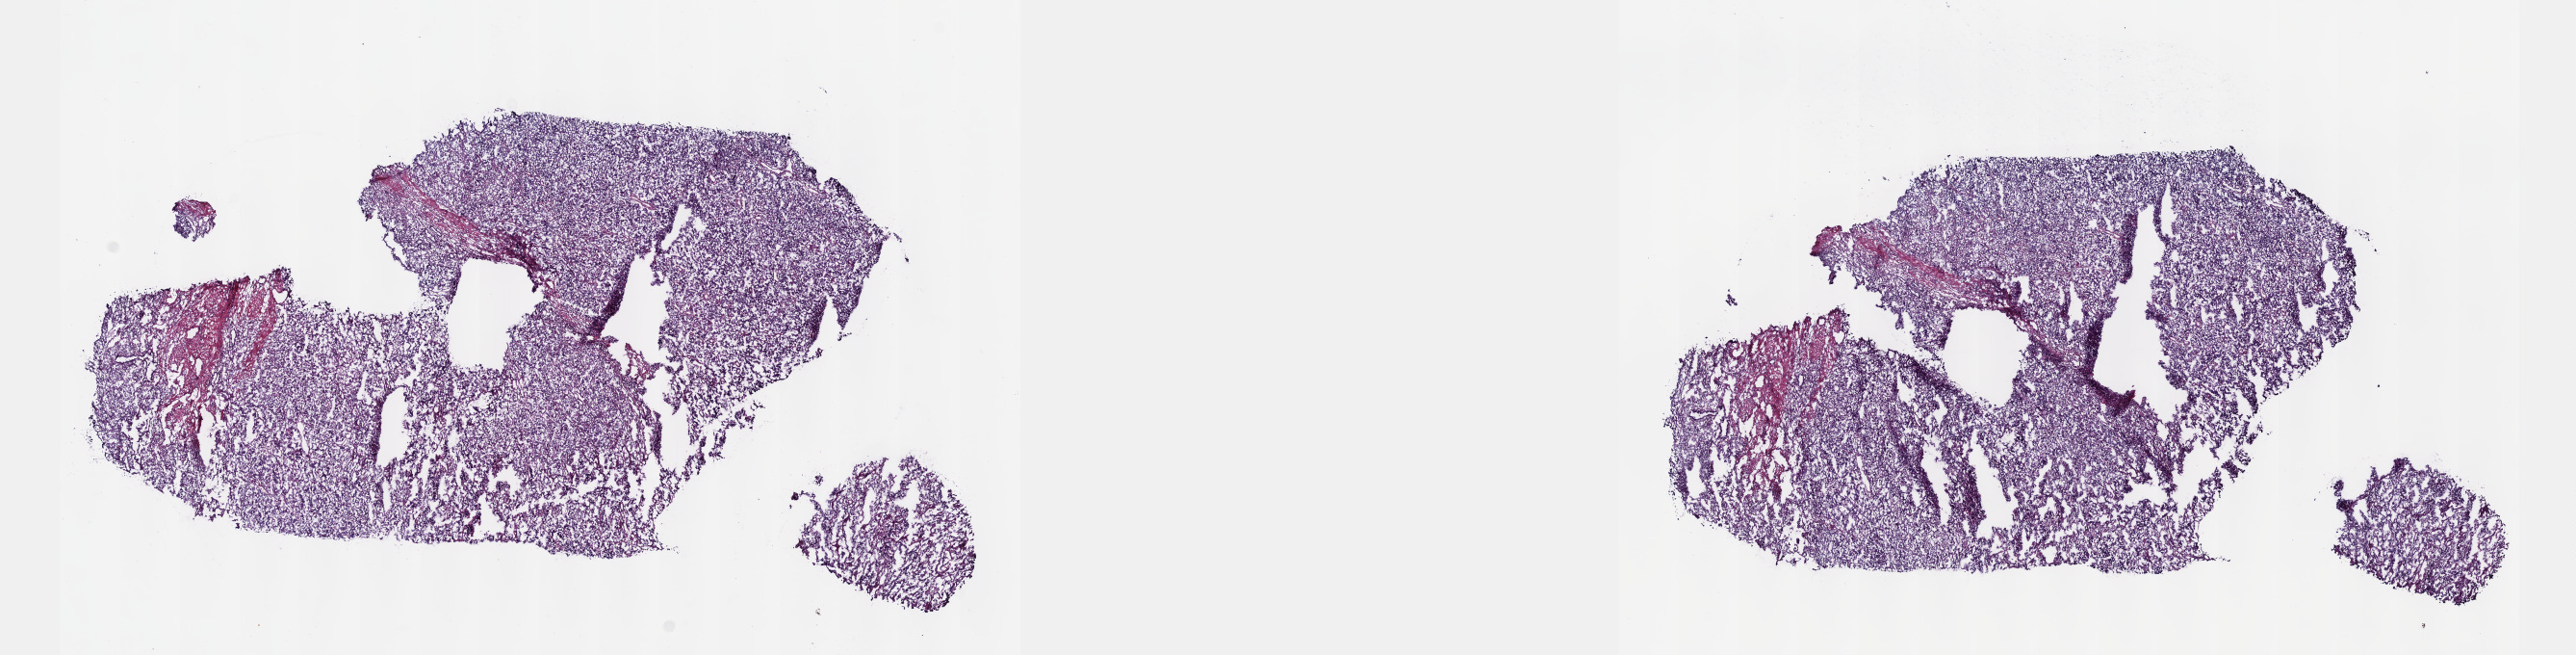
Whole-slide histology image, Hematoxylin and eosin (H&E) stained — low-resolution overview of the scanned area, about 21.6 x 5.5 mm (acquisition: 40x scan). Frozen section from the top of the tissue portion. Uterus, primary tumour sample. Patient: female, age at initial diagnosis 61 years. Composition of this section per pathologist review: tumour cells 70%, tumour nuclei 70%.
Diagnosis: Serous cystadenocarcinoma, NOS (endometrium).